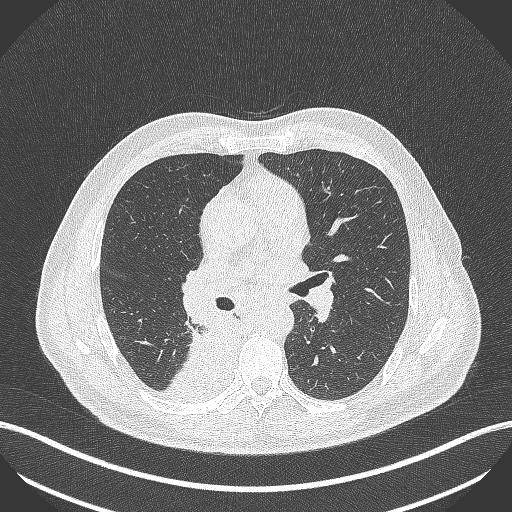
Chest CT, one axial slice. Reconstruction kernel B70f. 100 kVp. Lung window (W 1500 / L -600 HU). 512 × 512 image matrix, field of view 400 × 400 mm. Patient: male, 61 years. From the clinical record (not read from this slice): clinical TNM (as recorded): T1 N0 M0.
Outlined on this slice (bounding box drawn by a radiologist):
- lung tumour (recorded histology: small cell carcinoma): box from (x=164, y=305) to (x=242, y=411) px